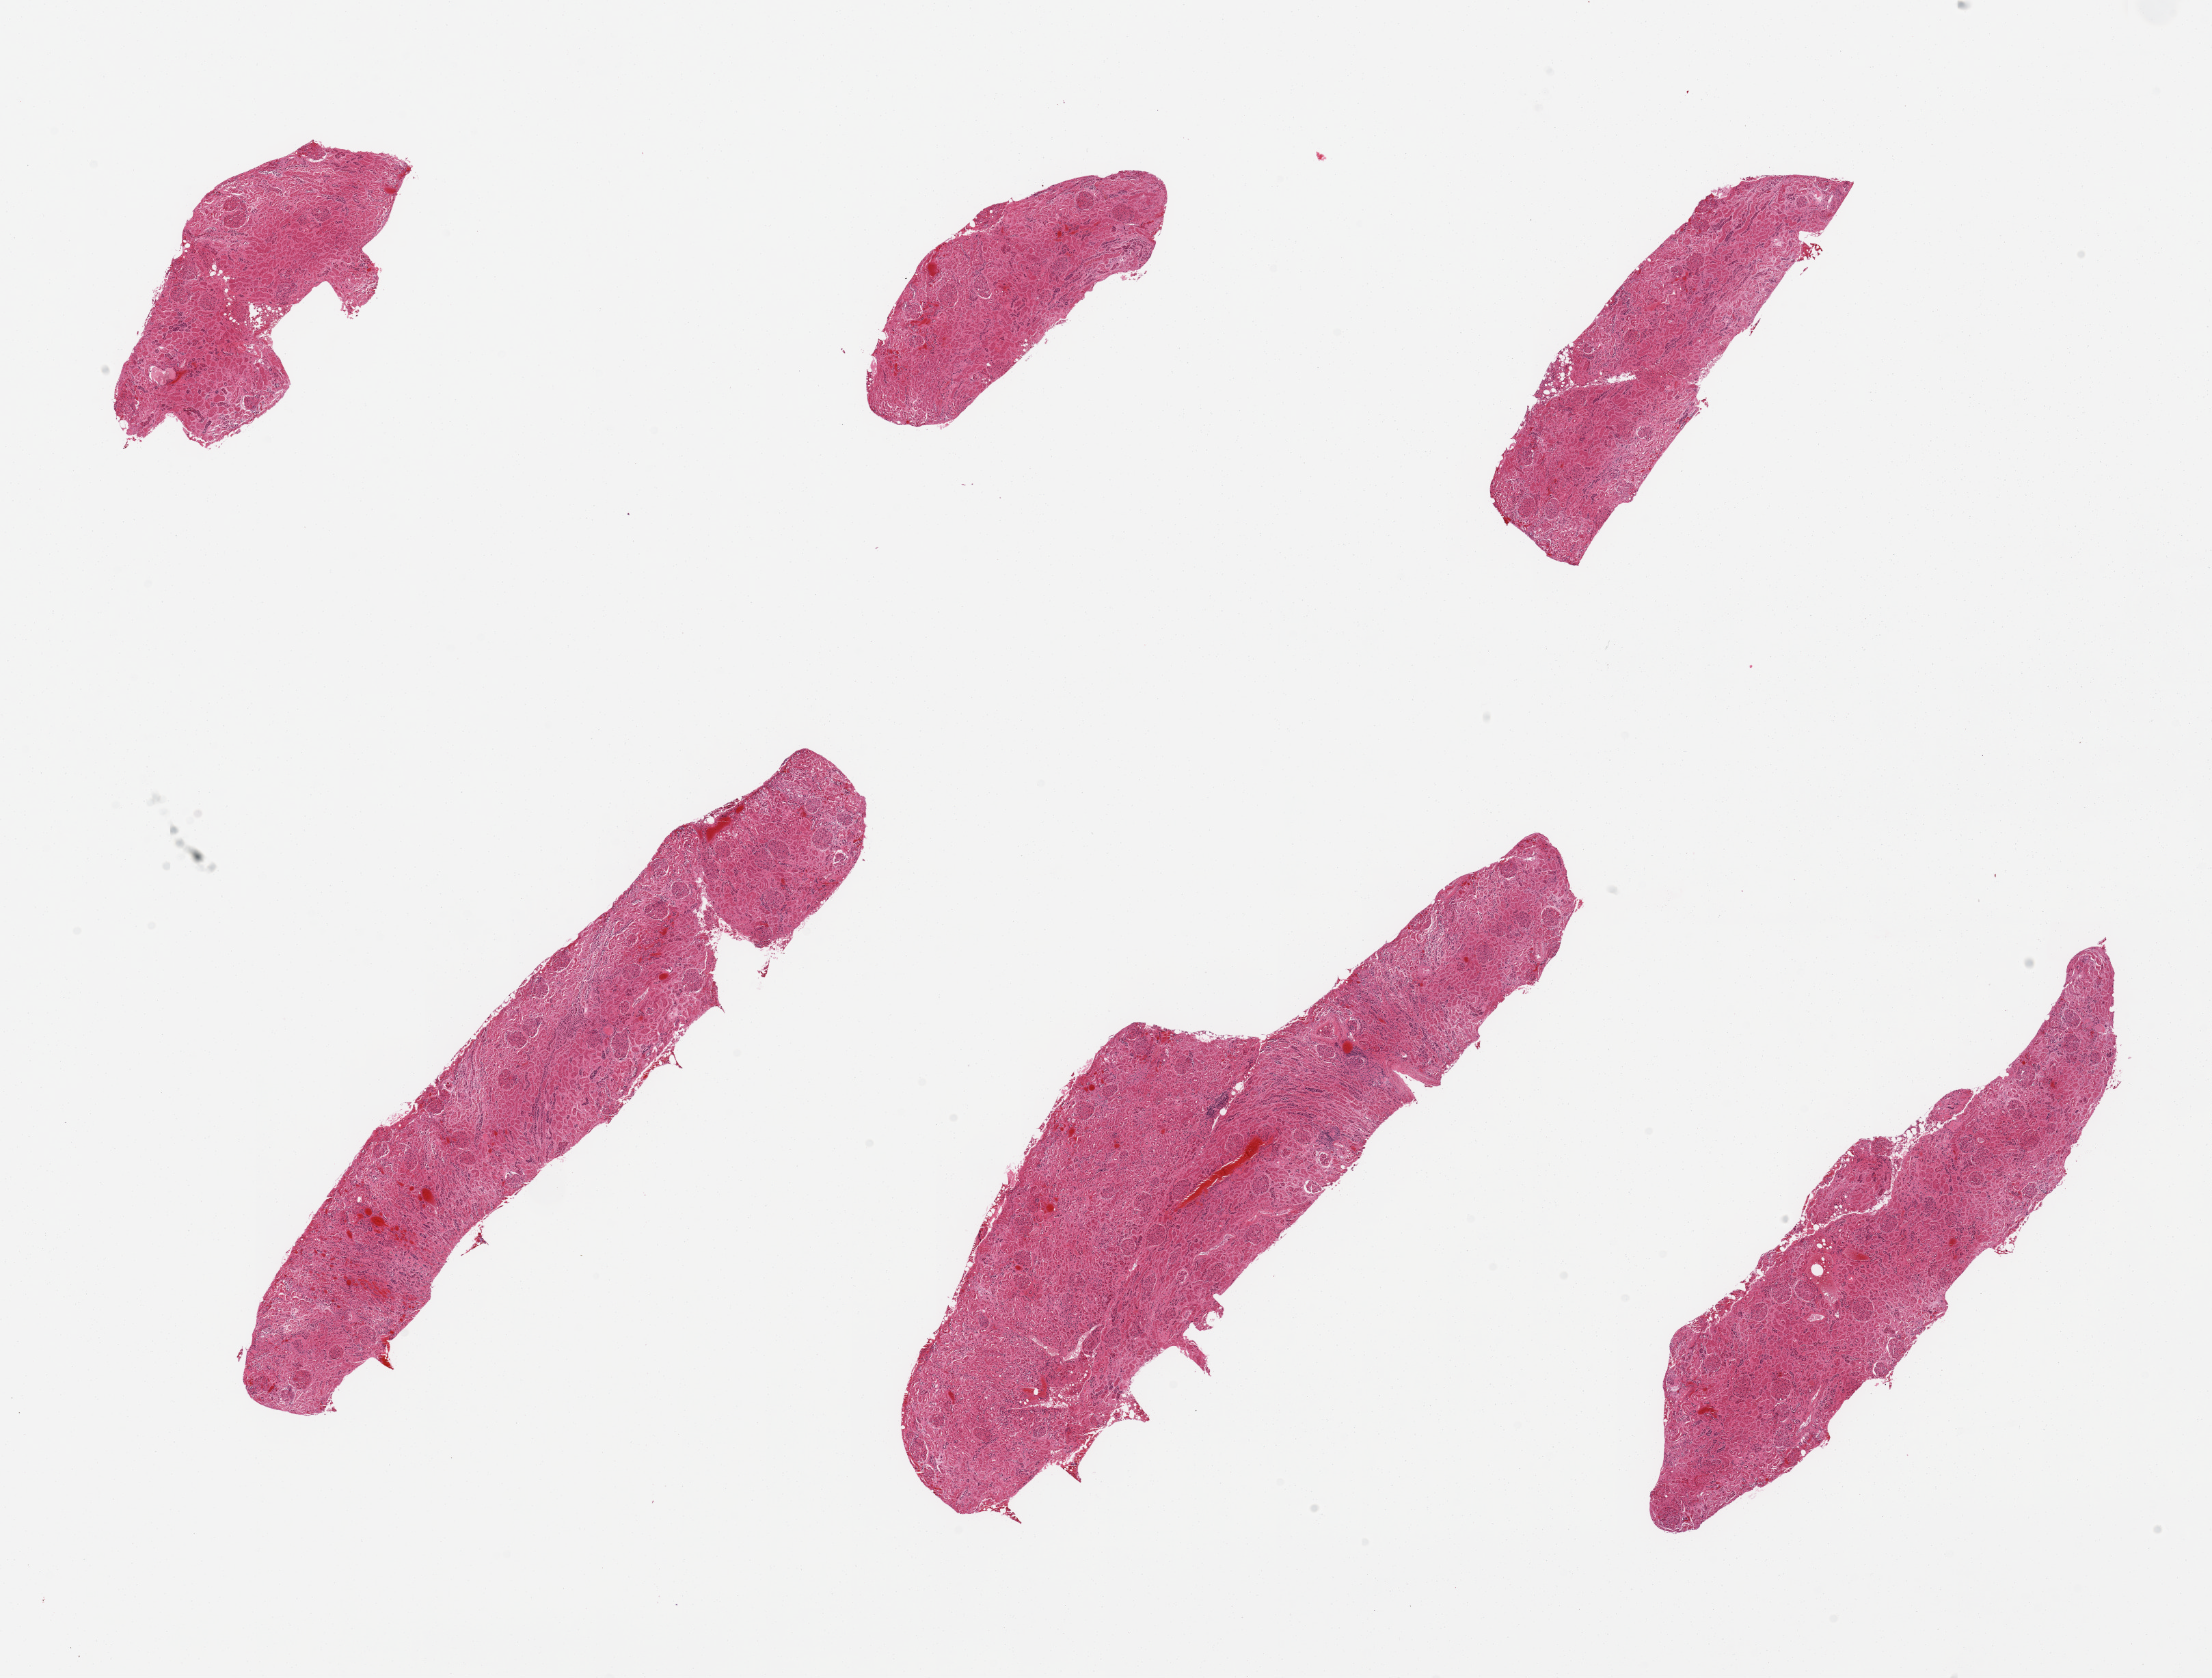
Digitized H&E-stained section — shown as a low-resolution overview of the whole scanned area (about 25.6 x 19.4 mm); PAXgene-fixed, paraffin-embedded tissue; target tissue: renal cortex; tissue donor sample. Male donor.
Reviewer comment on this tissue sample: 6 pieces, glomeruli in all sections.